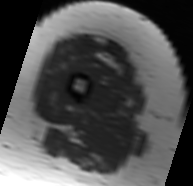
MRI of an extremity soft-tissue mass, one axial slice. MR volume resampled by the dataset authors to the PET/CT grid (not the native acquisition matrix). 3.27 mm slice thickness. 193 × 186 image matrix. Female patient. From the clinical record (not read from this slice): histological type: malignant solitary fibrous tumor; grade: intermediate; site of the primary tumour: right thigh.
Annotated regions visible in this slice (expert contour drawn on MRI and transferred to this co-registered scan by the dataset authors):
- gross tumour volume including surrounding oedema: bounding box <70,37,125,75> (left, top, right, bottom; pixels)